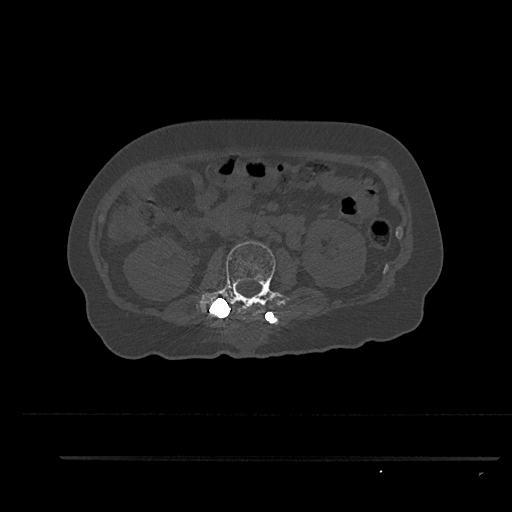
CT including the spine, one axial slice; 120 kVp; bone window (W 1800 / L 400 HU); 512 × 512 image matrix, field of view 408 × 408 mm. Patient: female, 44 years. From the clinical record (not read from this slice): primary cancer: renal.
Structures marked on this image (semi-automatic segmentation, software-assisted and operator-edited):
- L2 vertebra: box from (x=196, y=241) to (x=284, y=319) px